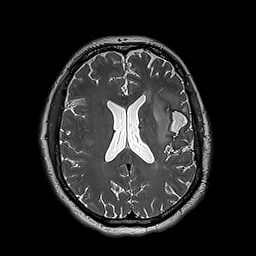
Brain MRI from a brain-tumour surgery series, one axial slice. Slice 88 of 192 in the series (ordered by position). 256 × 256 image matrix, field of view 250 × 250 mm. Case-level facts recorded for this patient, not image findings: histopathology: Astrocytoma; WHO grade: 3; IDH mutation: yes; tumour location: Left Insular.
Outlined on this slice (expert manual segmentation):
- tumour: box from (x=153, y=92) to (x=180, y=145) px